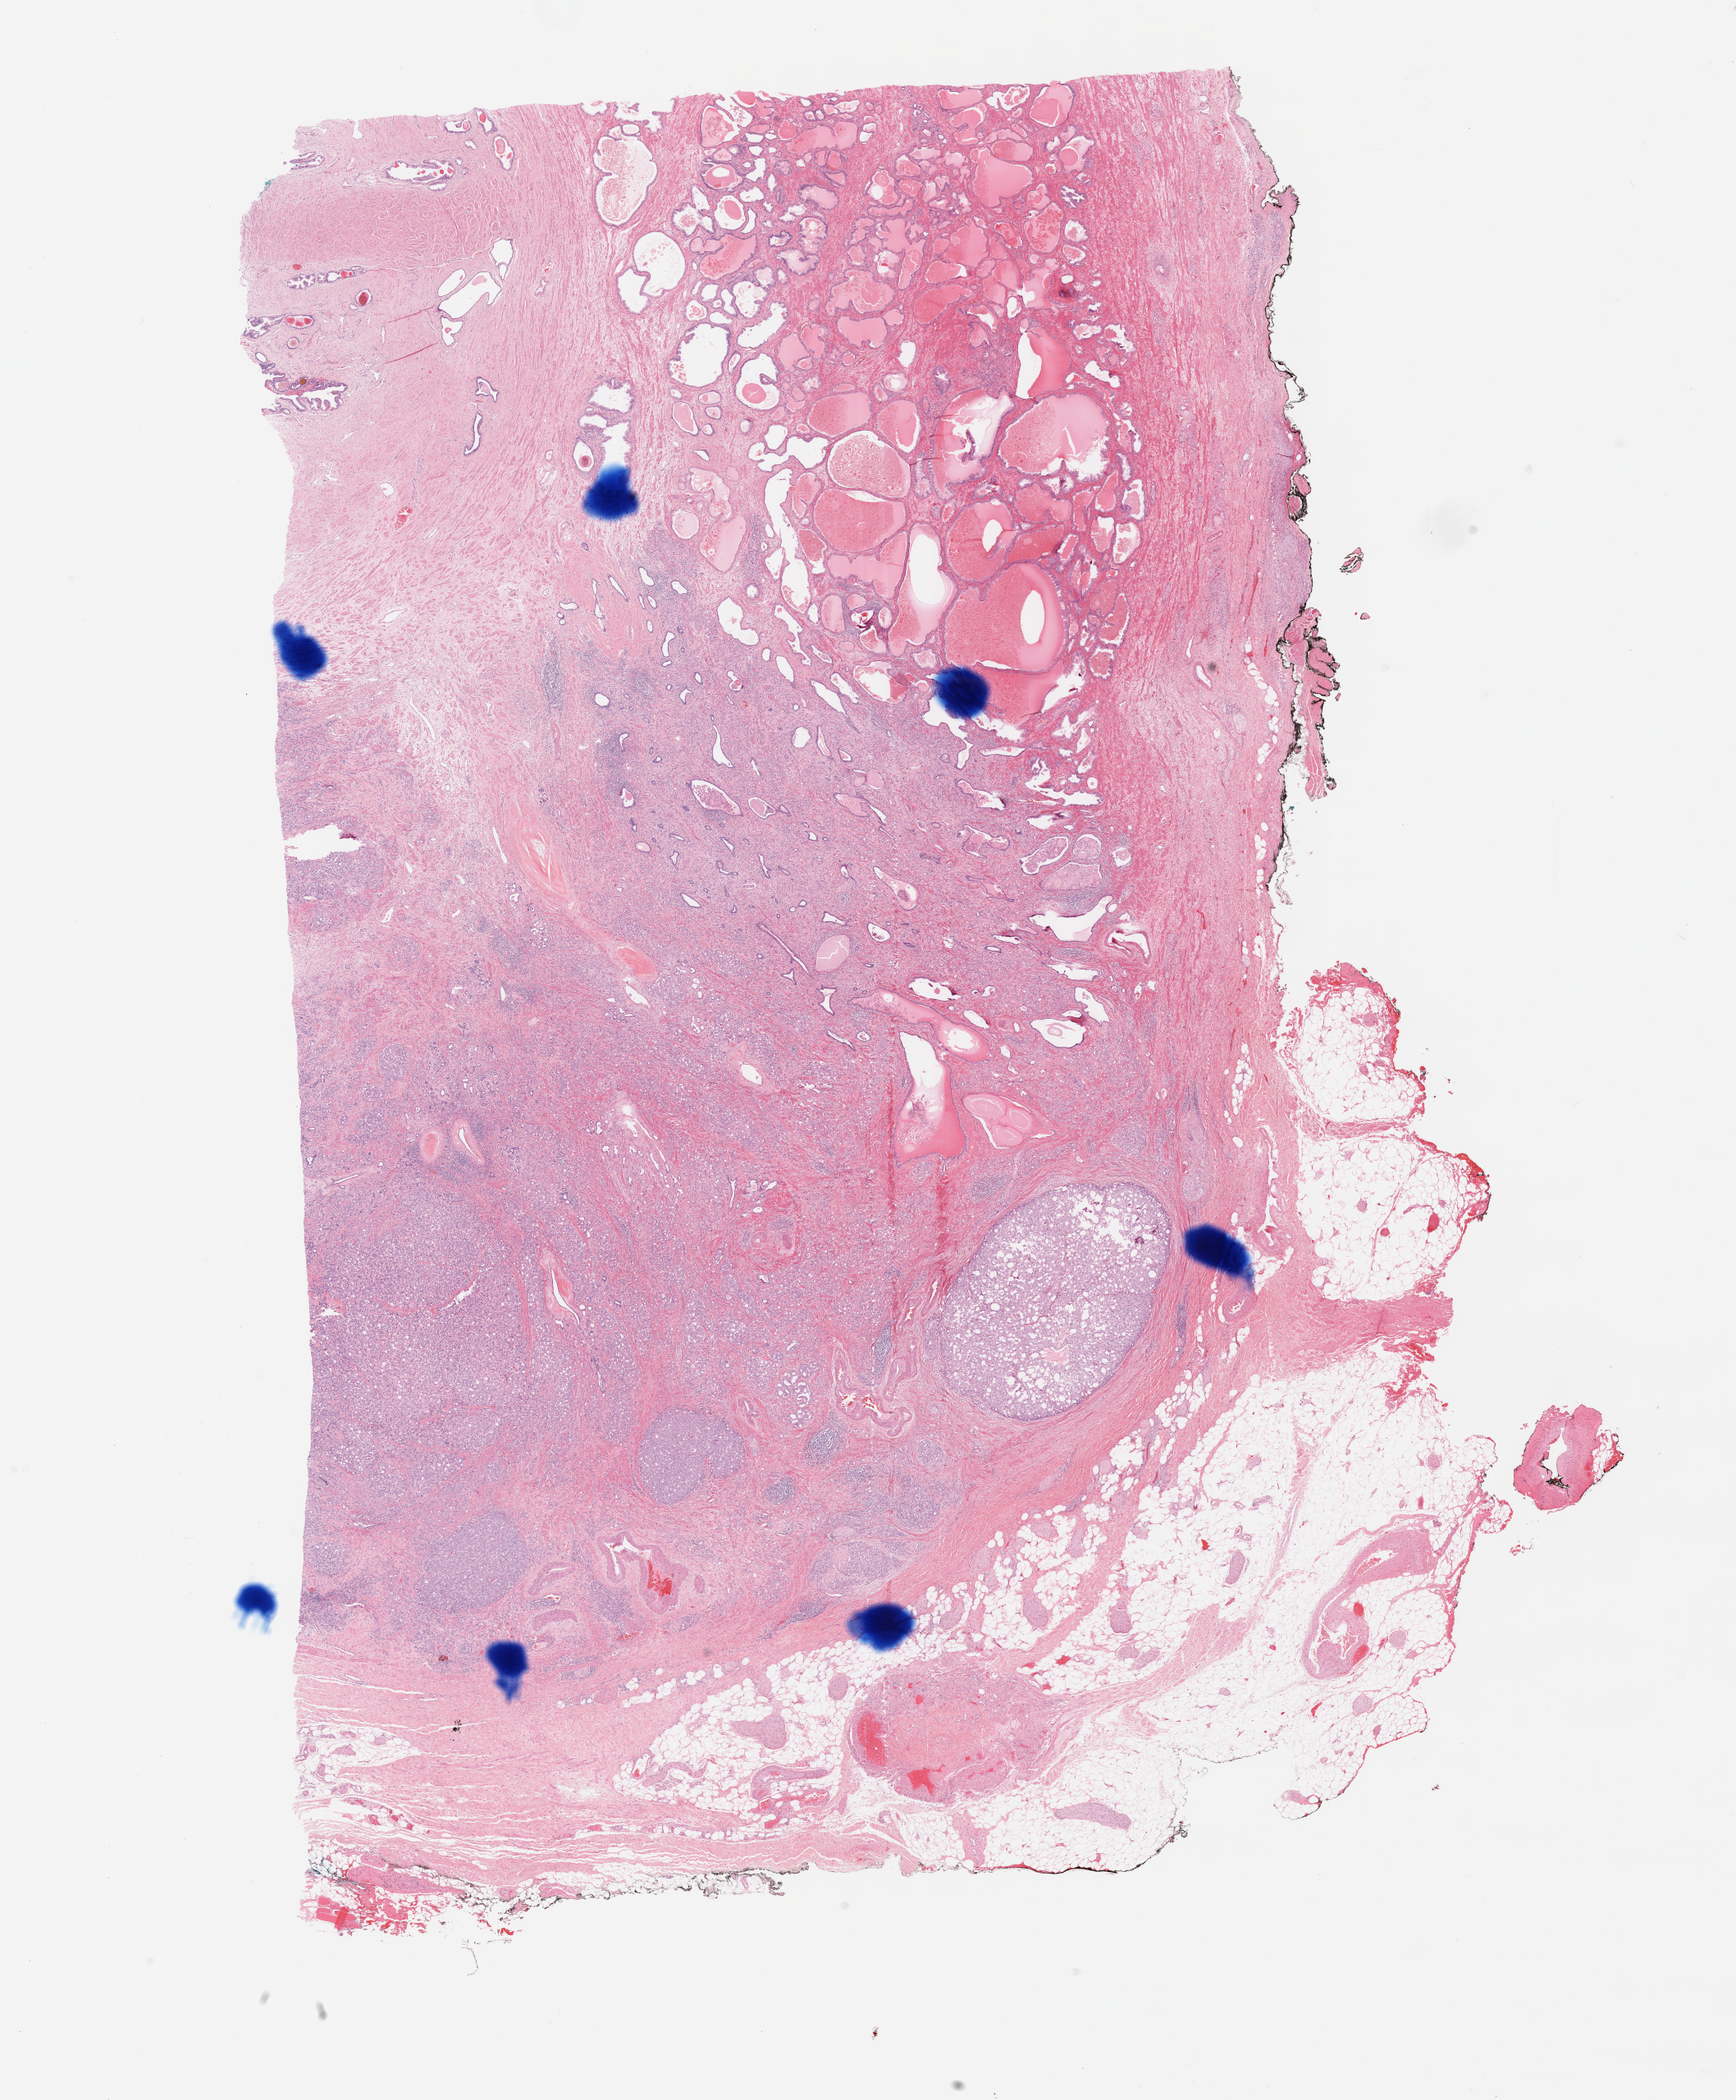
Digitized H&E-stained tissue section (whole slide) — shown as a low-resolution overview of the whole scanned area (about 17.1 x 20.7 mm, acquisition: 40x scan), formalin-fixed paraffin-embedded (FFPE) diagnostic section, prostate, primary tumour sample. Male patient; age at initial diagnosis 65 years. Gleason score: 9 (5+4).
Laterality: bilateral. Lymph nodes positive (case pathology): 0 of 9 examined. Pathologic diagnosis: Adenocarcinoma, NOS (prostate gland).